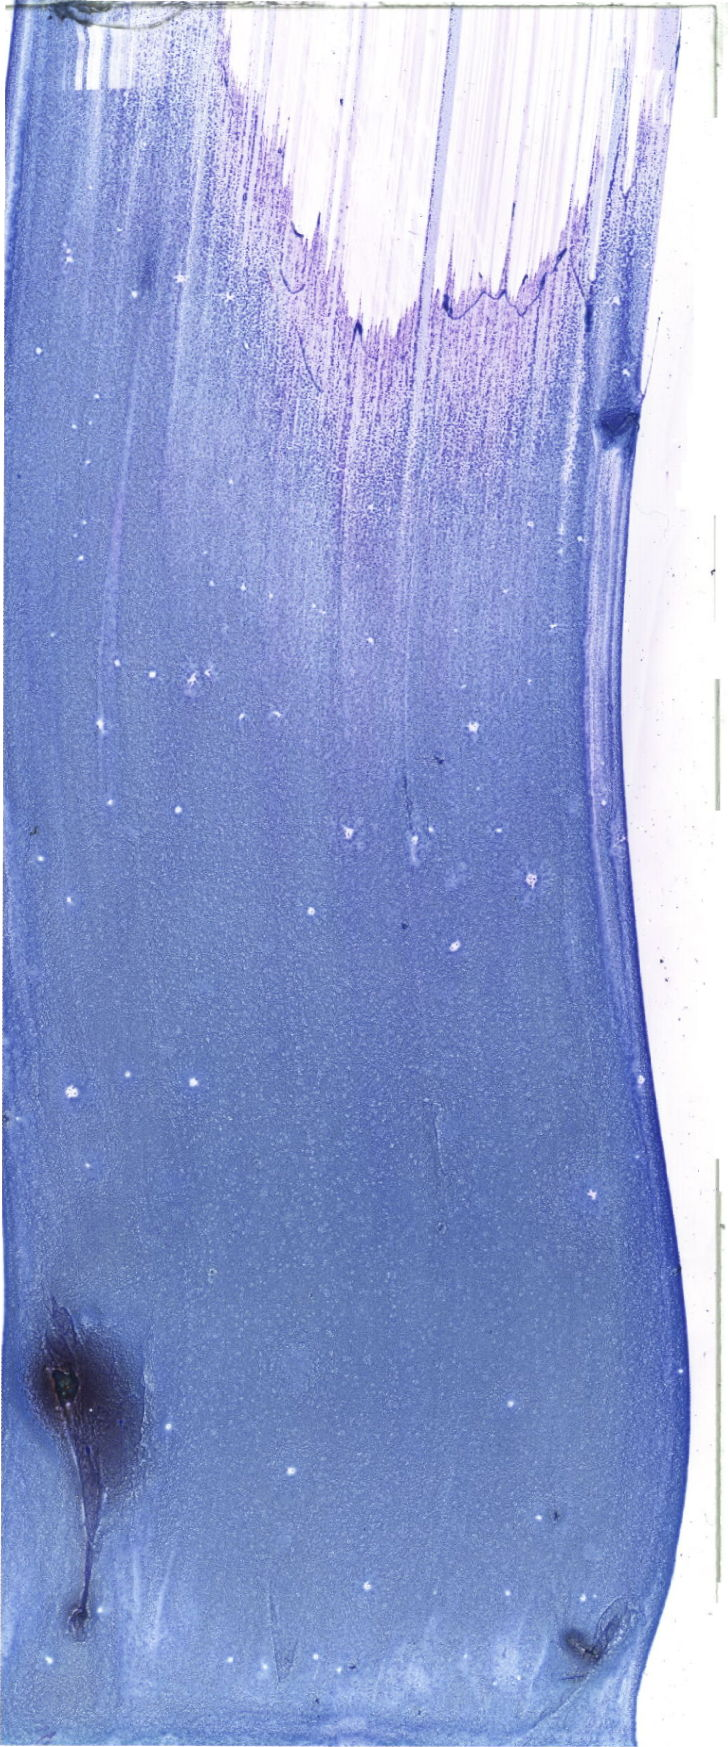
May-Grünwald-Giemsa (MGG)-stained marrow aspirate smear (whole slide) — low-resolution overview of the scanned area, about 20.6 x 49.5 mm. Patient sex: male.
- diagnosis: Acute Promyelocytic Leukemia with t(15;17)(q24.1;q21.2);PML-RARA